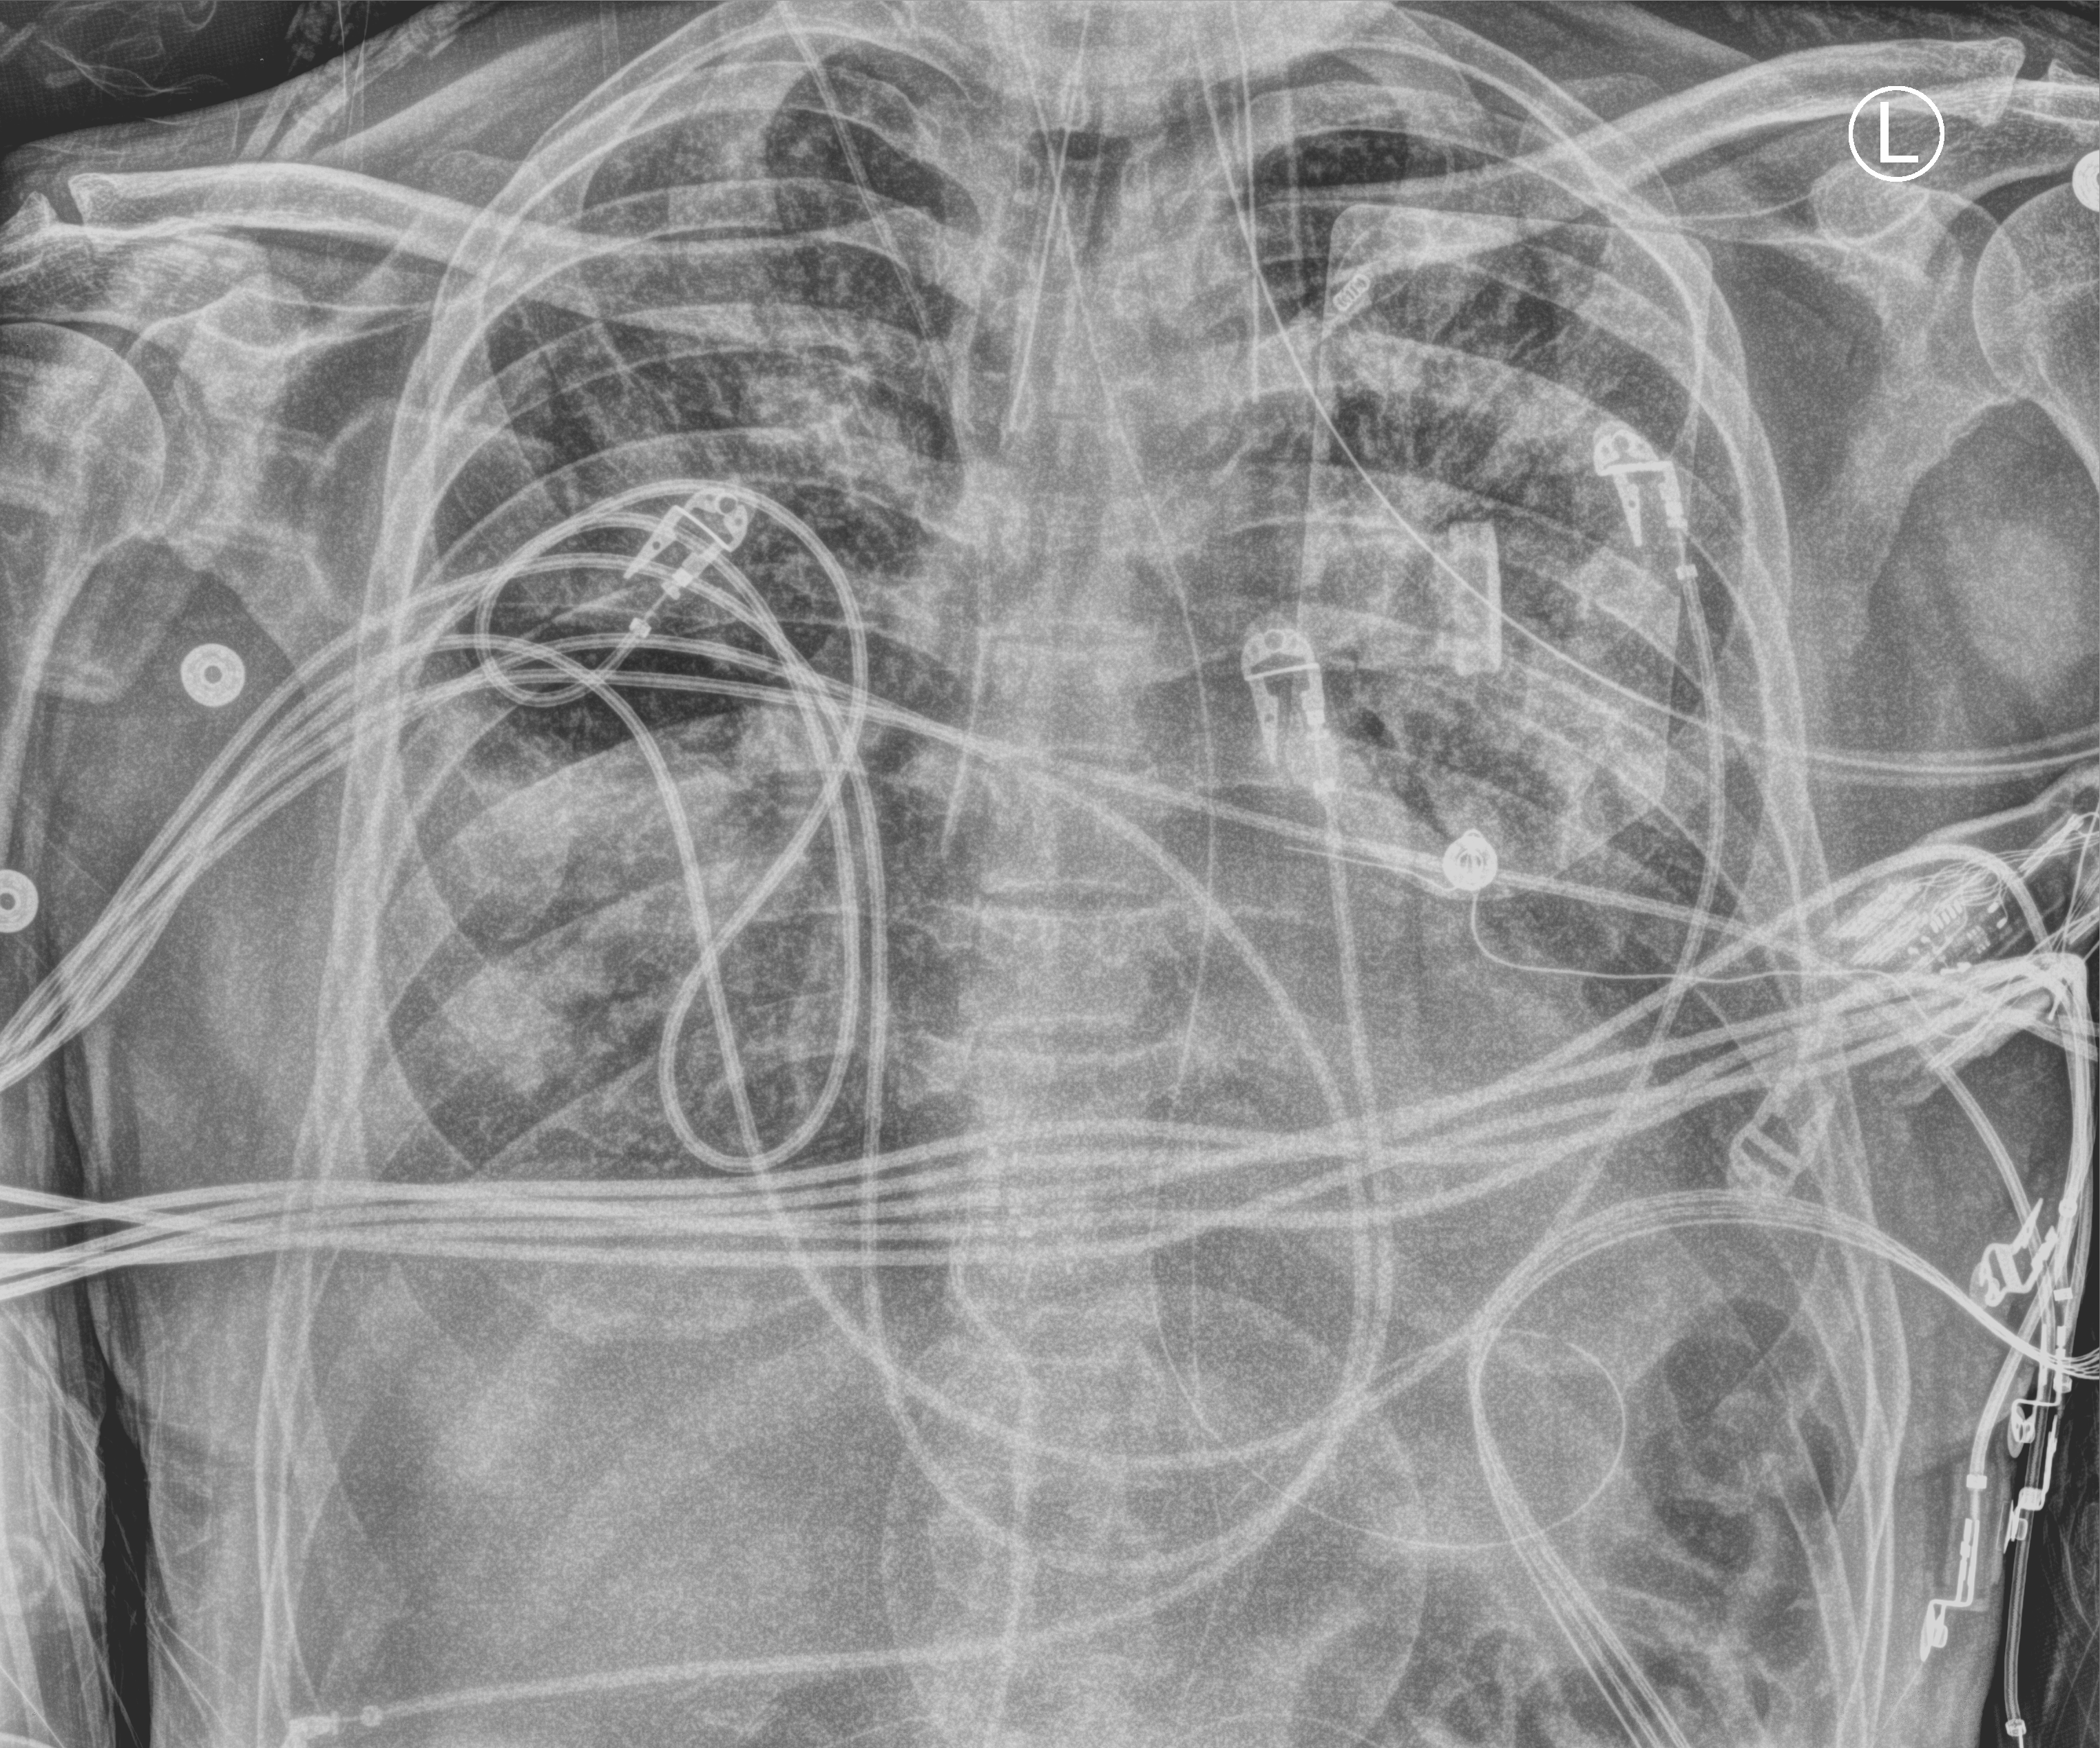
Portable chest radiograph. Male patient hospitalised with COVID-19, age 60–74 years.
From the hospital-stay record, not from the radiograph (when in the stay this image was taken is not recorded): admitted to intensive care during this hospital stay: yes.